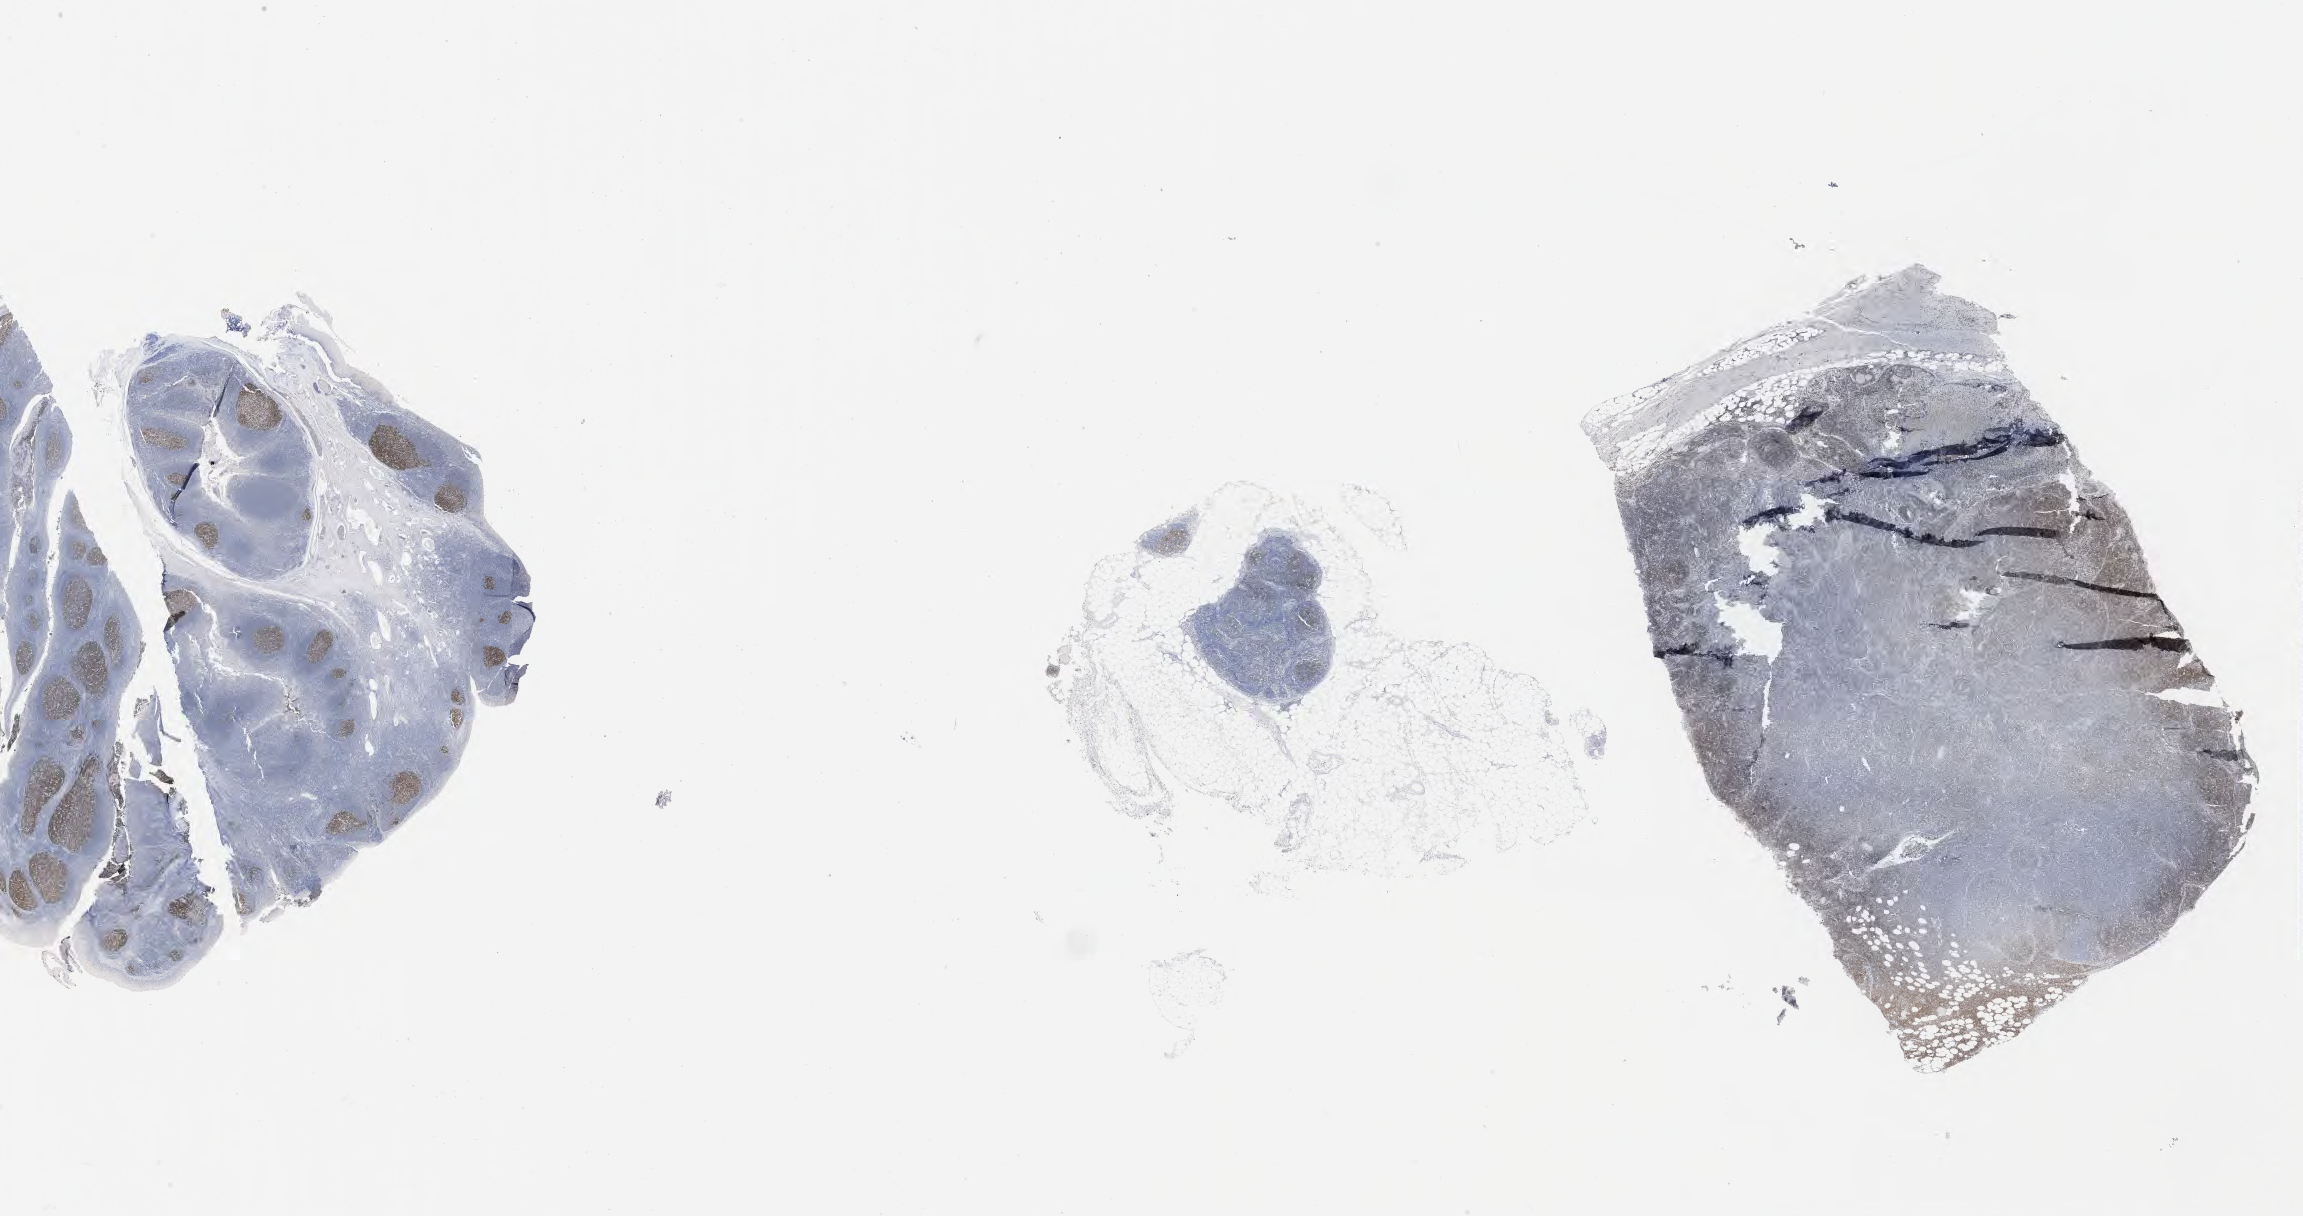
Immunohistochemistry (IHC) whole-slide image stained for BCL6, shown as a low-resolution overview of the whole scanned area (about 37.2 x 19.7 mm); tumor tissue. Male patient, 40 years old.
Diagnosis: Burkitt lymphoma, NOS.